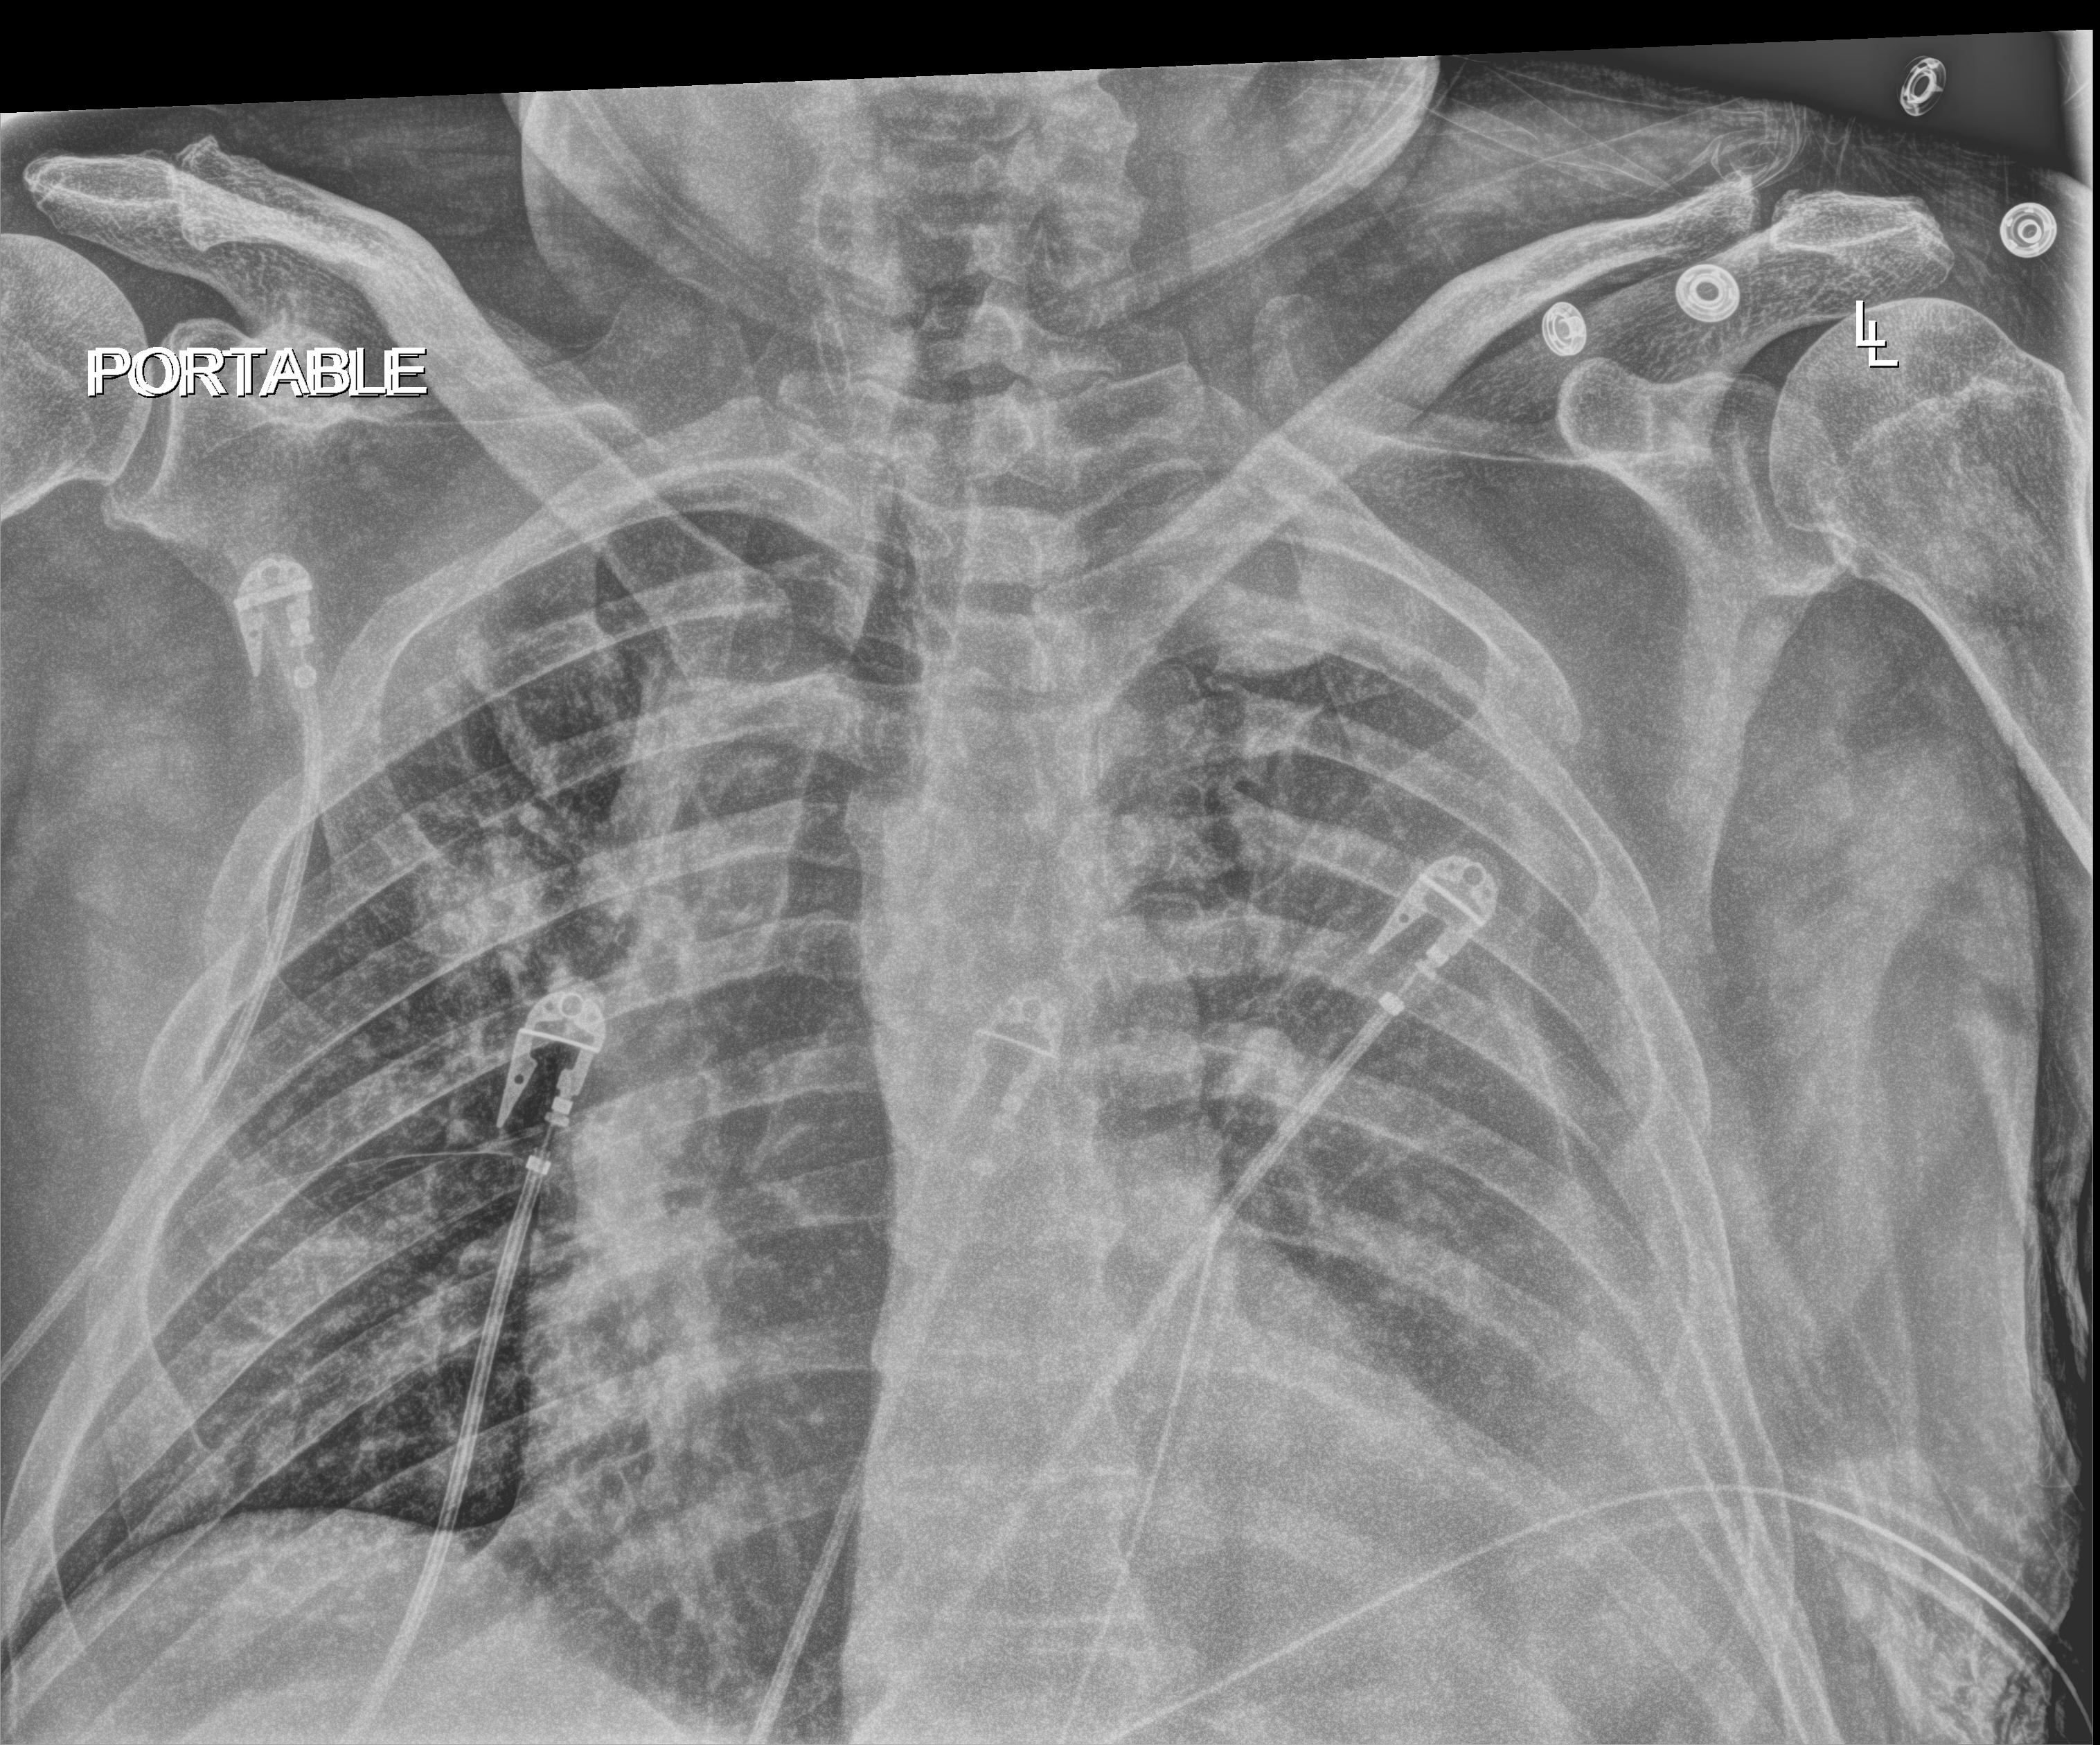
Chest X-ray (portable); anteroposterior (AP) projection. Male patient hospitalised with COVID-19, age 18–59 years.
From the hospital-stay record, not from the radiograph (when in the stay this image was taken is not recorded): mechanically ventilated during this hospital stay: no; admitted to intensive care during this hospital stay: no; length of hospital stay: 10 days.